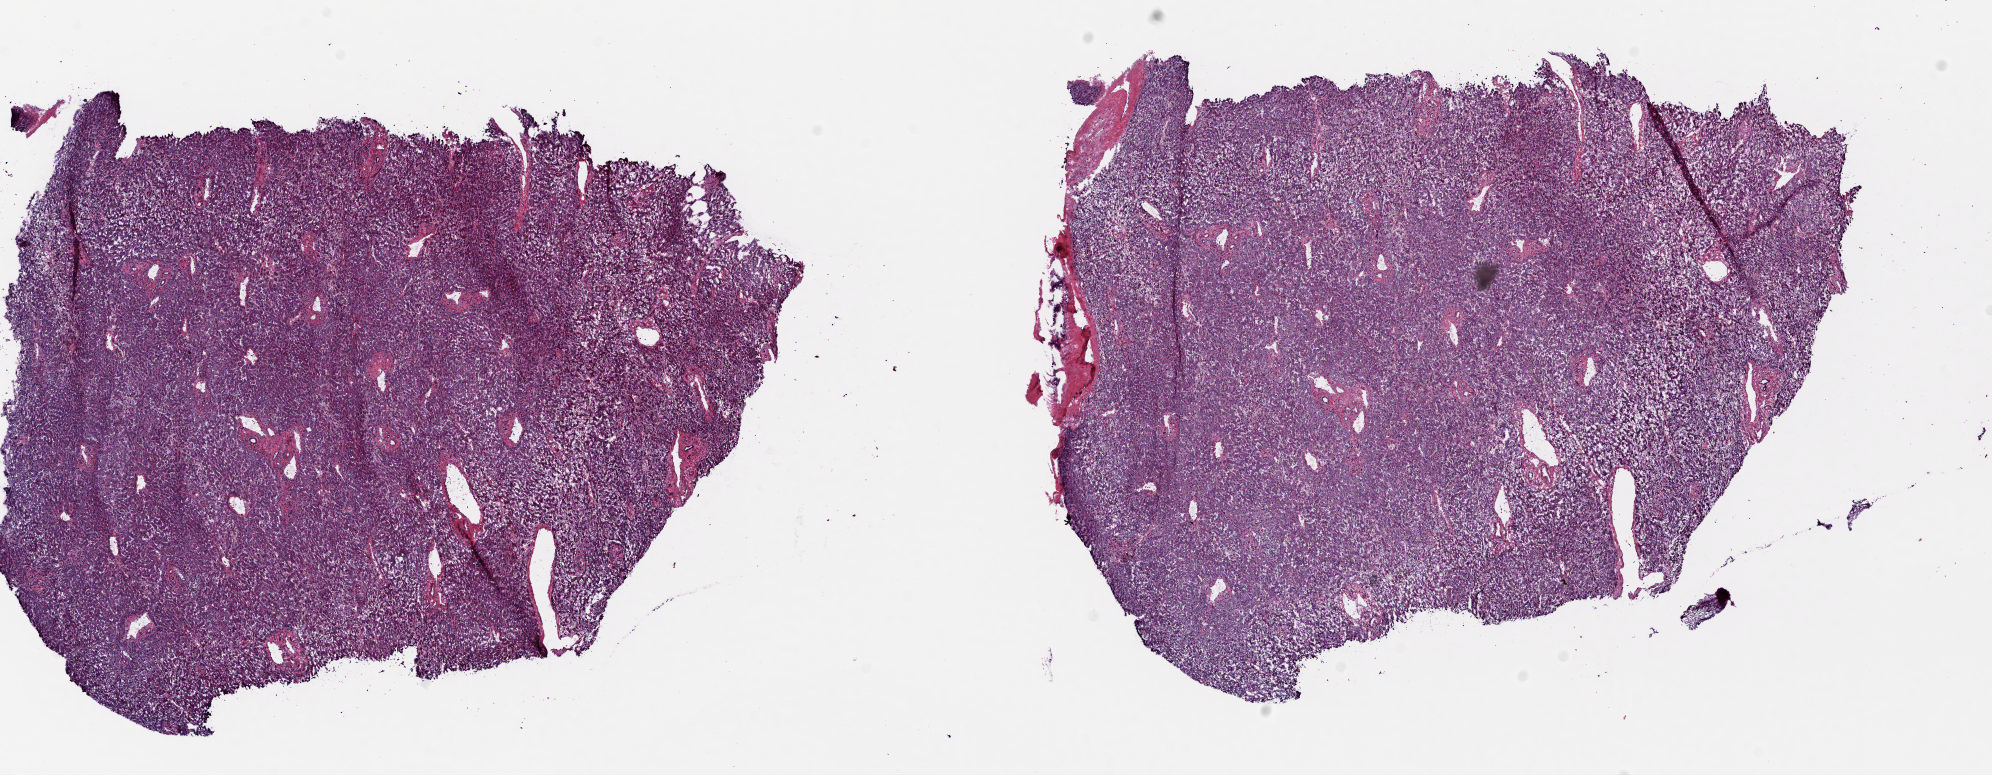
H&E-stained whole-slide image, low-resolution overview of the scanned area, about 15.8 x 6.2 mm (acquisition: 20x scan); frozen section from the top of the tissue portion; sample: solid tissue normal (non-tumour tissue), liver. Male, age 76 years at initial diagnosis. Slide review estimates, as recorded: tumour cells 0%, tumour nuclei 0%, normal cells 80%, stromal cells 20%, necrosis 0%. Infiltration values recorded for this section: lymphocyte infiltration 5%, monocyte infiltration 0%, neutrophil infiltration 0%.
This section: solid tissue normal (non-tumour) sample from the same patient. Patient diagnosis: Hepatocellular carcinoma, NOS.